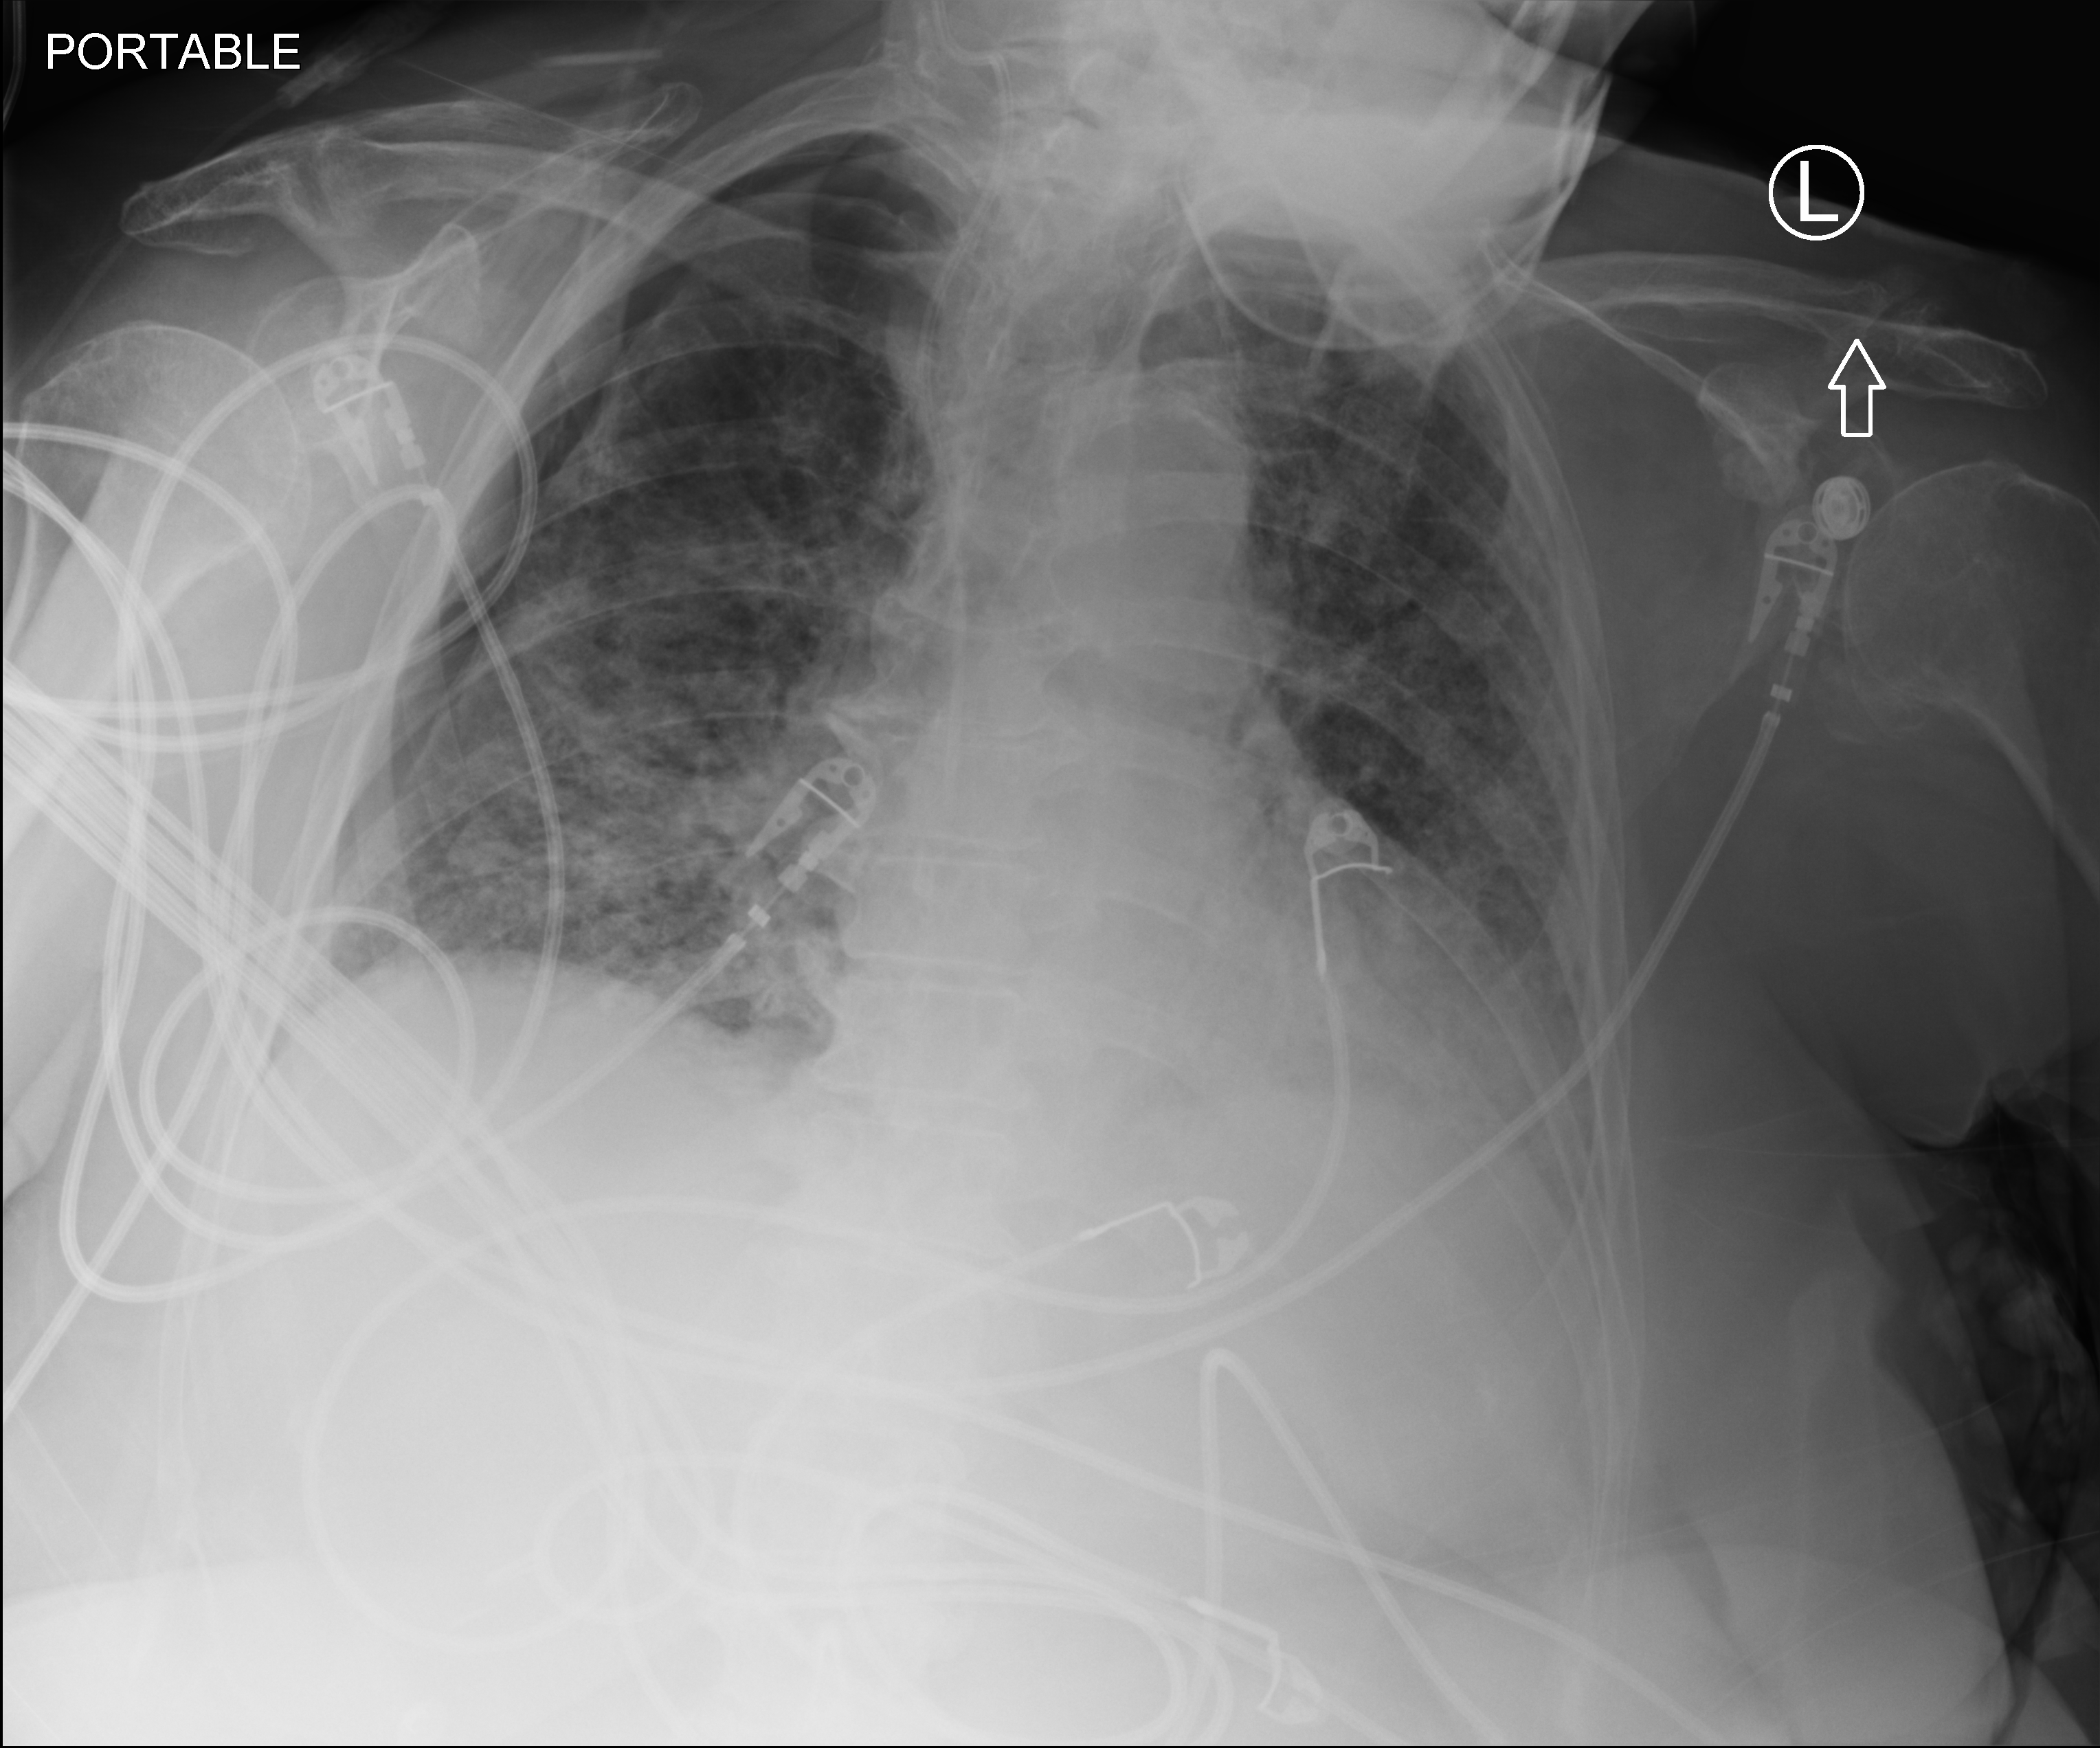
Portable chest radiograph; anteroposterior (AP) projection. Patient hospitalised with COVID-19; female, aged 75–90 years.
Admission-level facts for this patient (not findings on this image; timing relative to this image not recorded): admitted to intensive care during this hospital stay: no; mechanically ventilated during this hospital stay: yes.